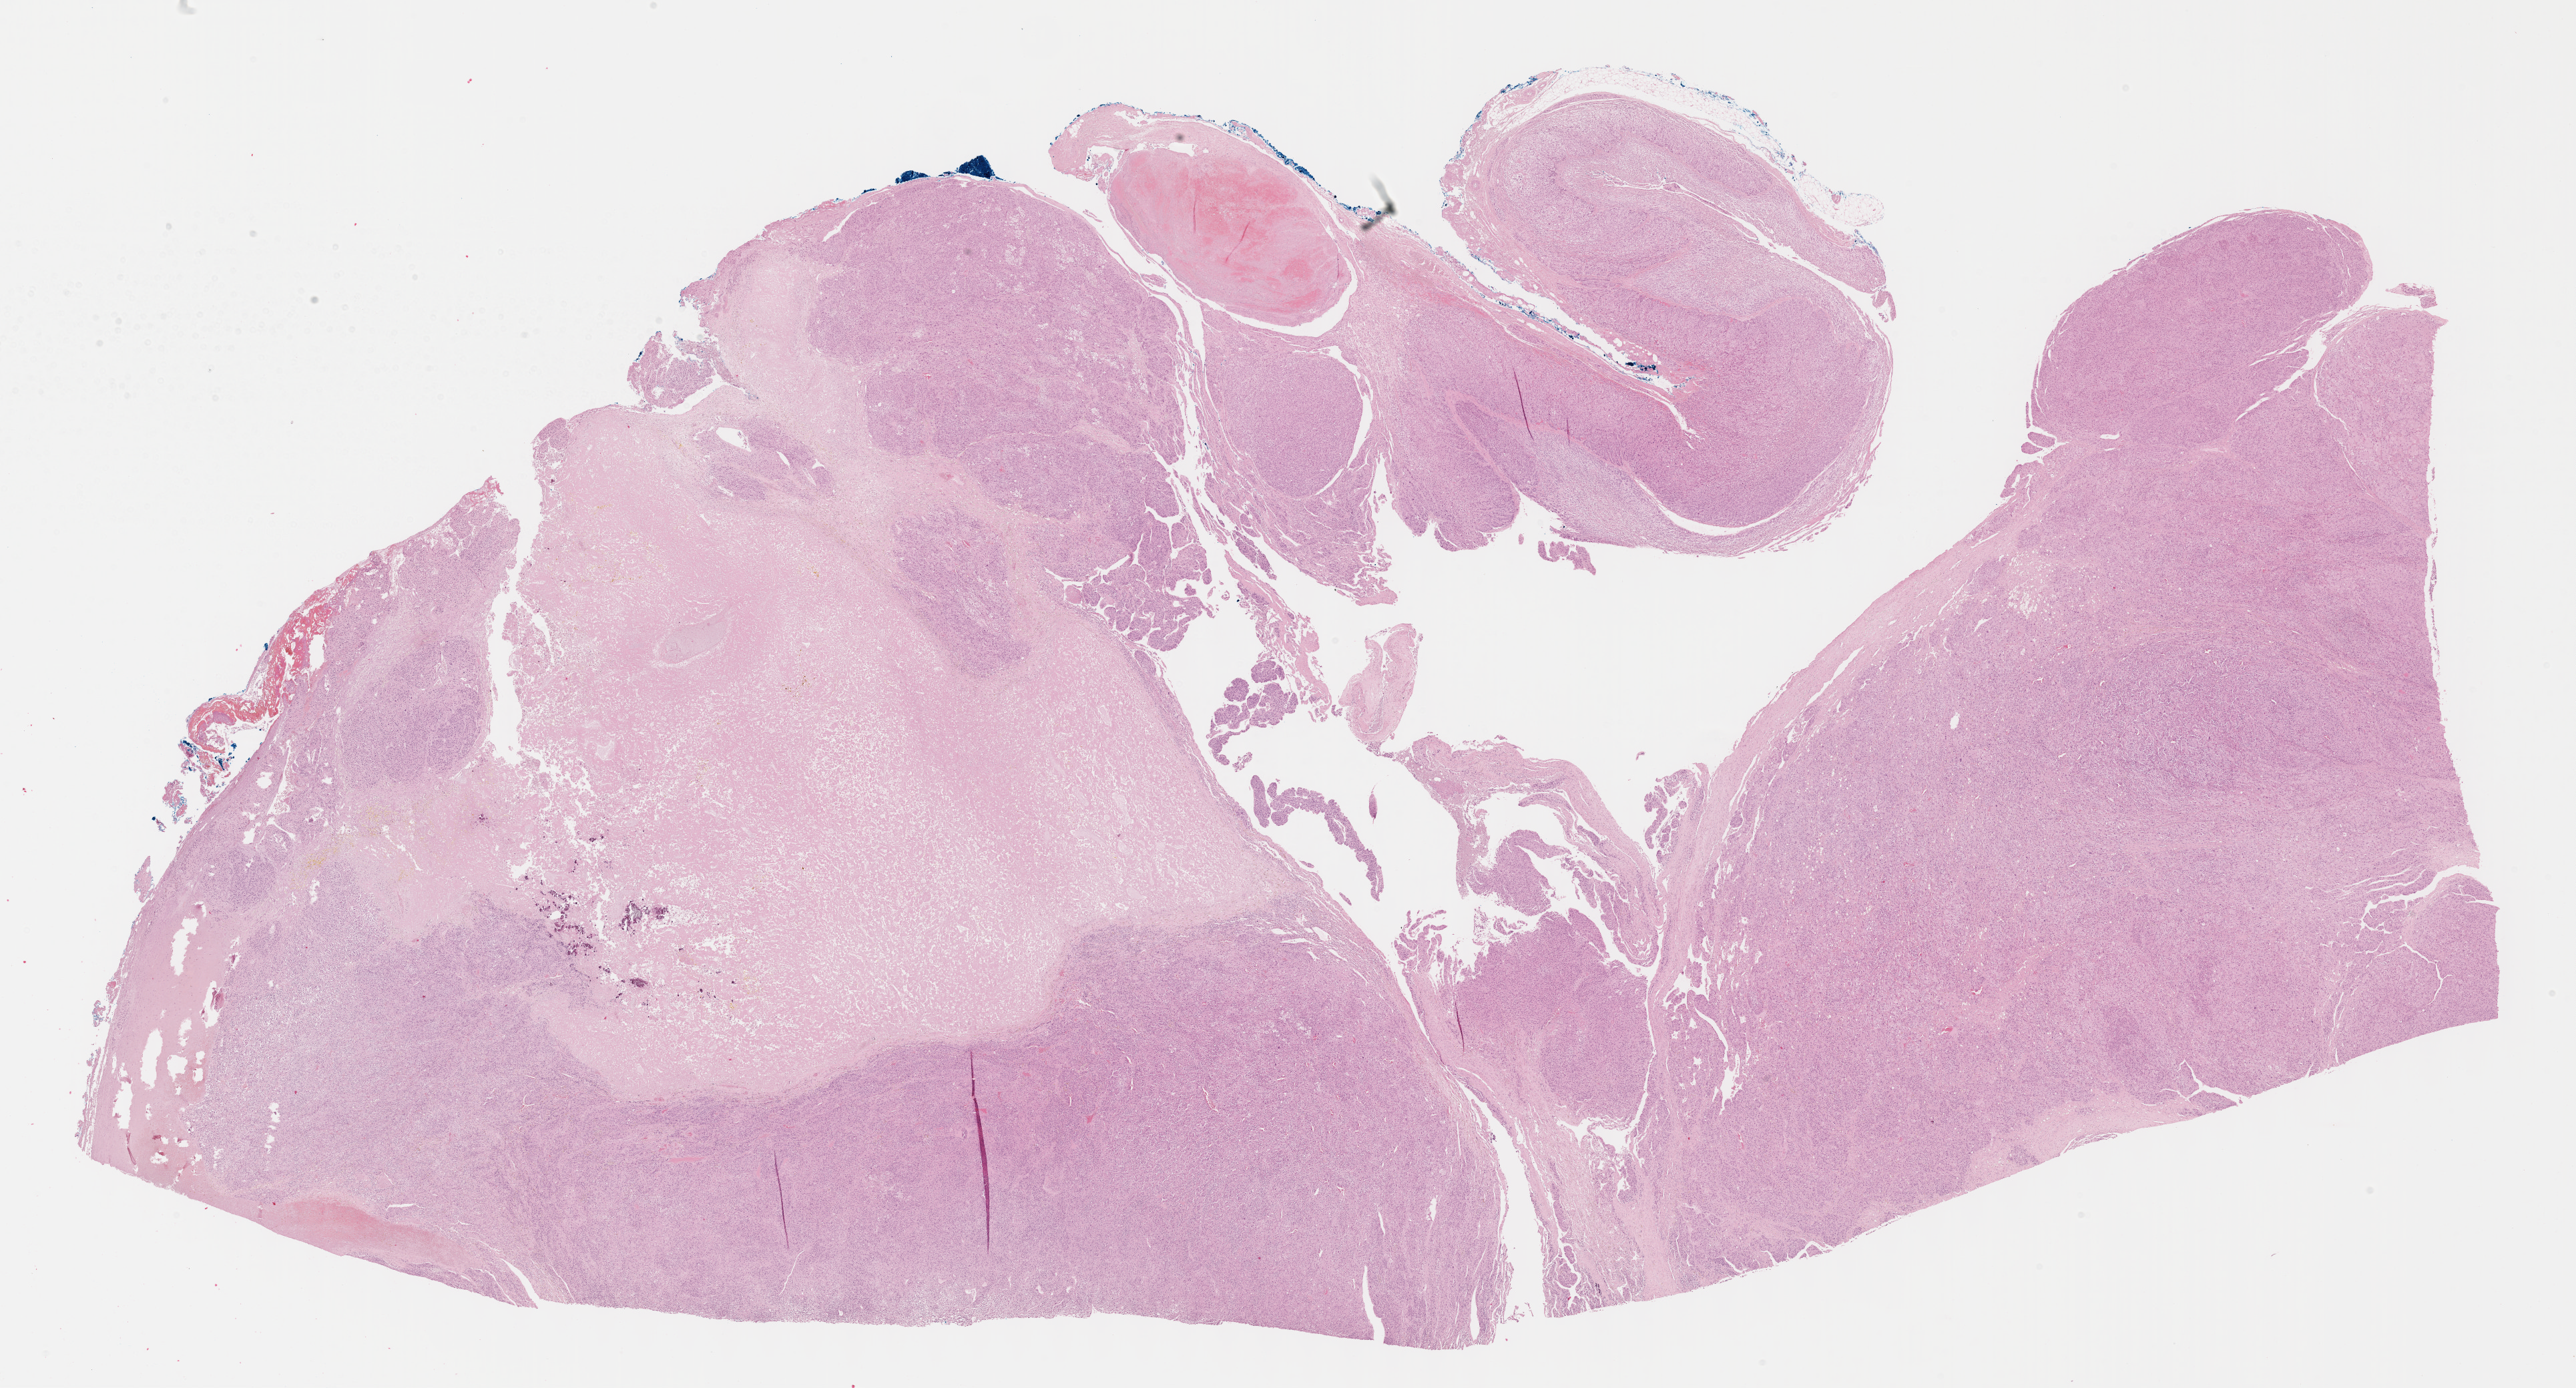
Digitized H&E-stained tissue section (whole slide) — shown as a low-resolution overview of the whole scanned area (about 31.2 x 16.8 mm, slide scanned at 40x); formalin-fixed paraffin-embedded (FFPE) diagnostic section; adrenal cortex, primary tumour sample. Female, age 17 years at initial diagnosis.
Diagnosis: Adrenal cortical carcinoma (cortex of adrenal gland).